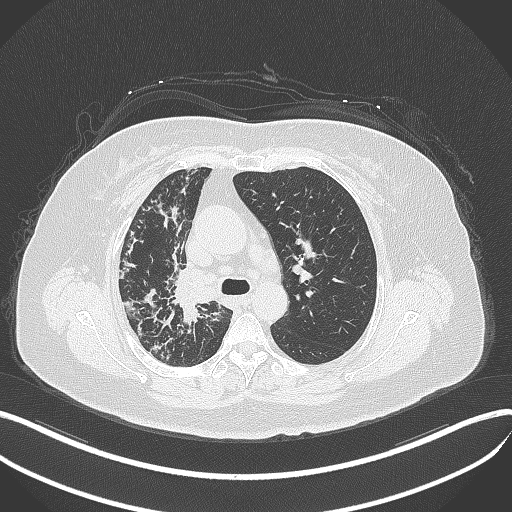
Chest CT, one axial slice; slice 242 of 376 in the series (ordered by position); reconstruction kernel B70f; 120 kVp; lung window (W 1500 / L -600 HU); 1 mm slice thickness; 512 × 512 image matrix. Patient: female, 60 years. Case-level facts recorded for this patient, not image findings: clinical TNM (as recorded): T1c N0 M0.
Annotated regions visible in this slice (rectangle marked by the reading radiologist):
- lung tumour (recorded histology: squamous cell carcinoma): bounding box (x1, y1, x2, y2) in pixels: (171, 261, 220, 309)